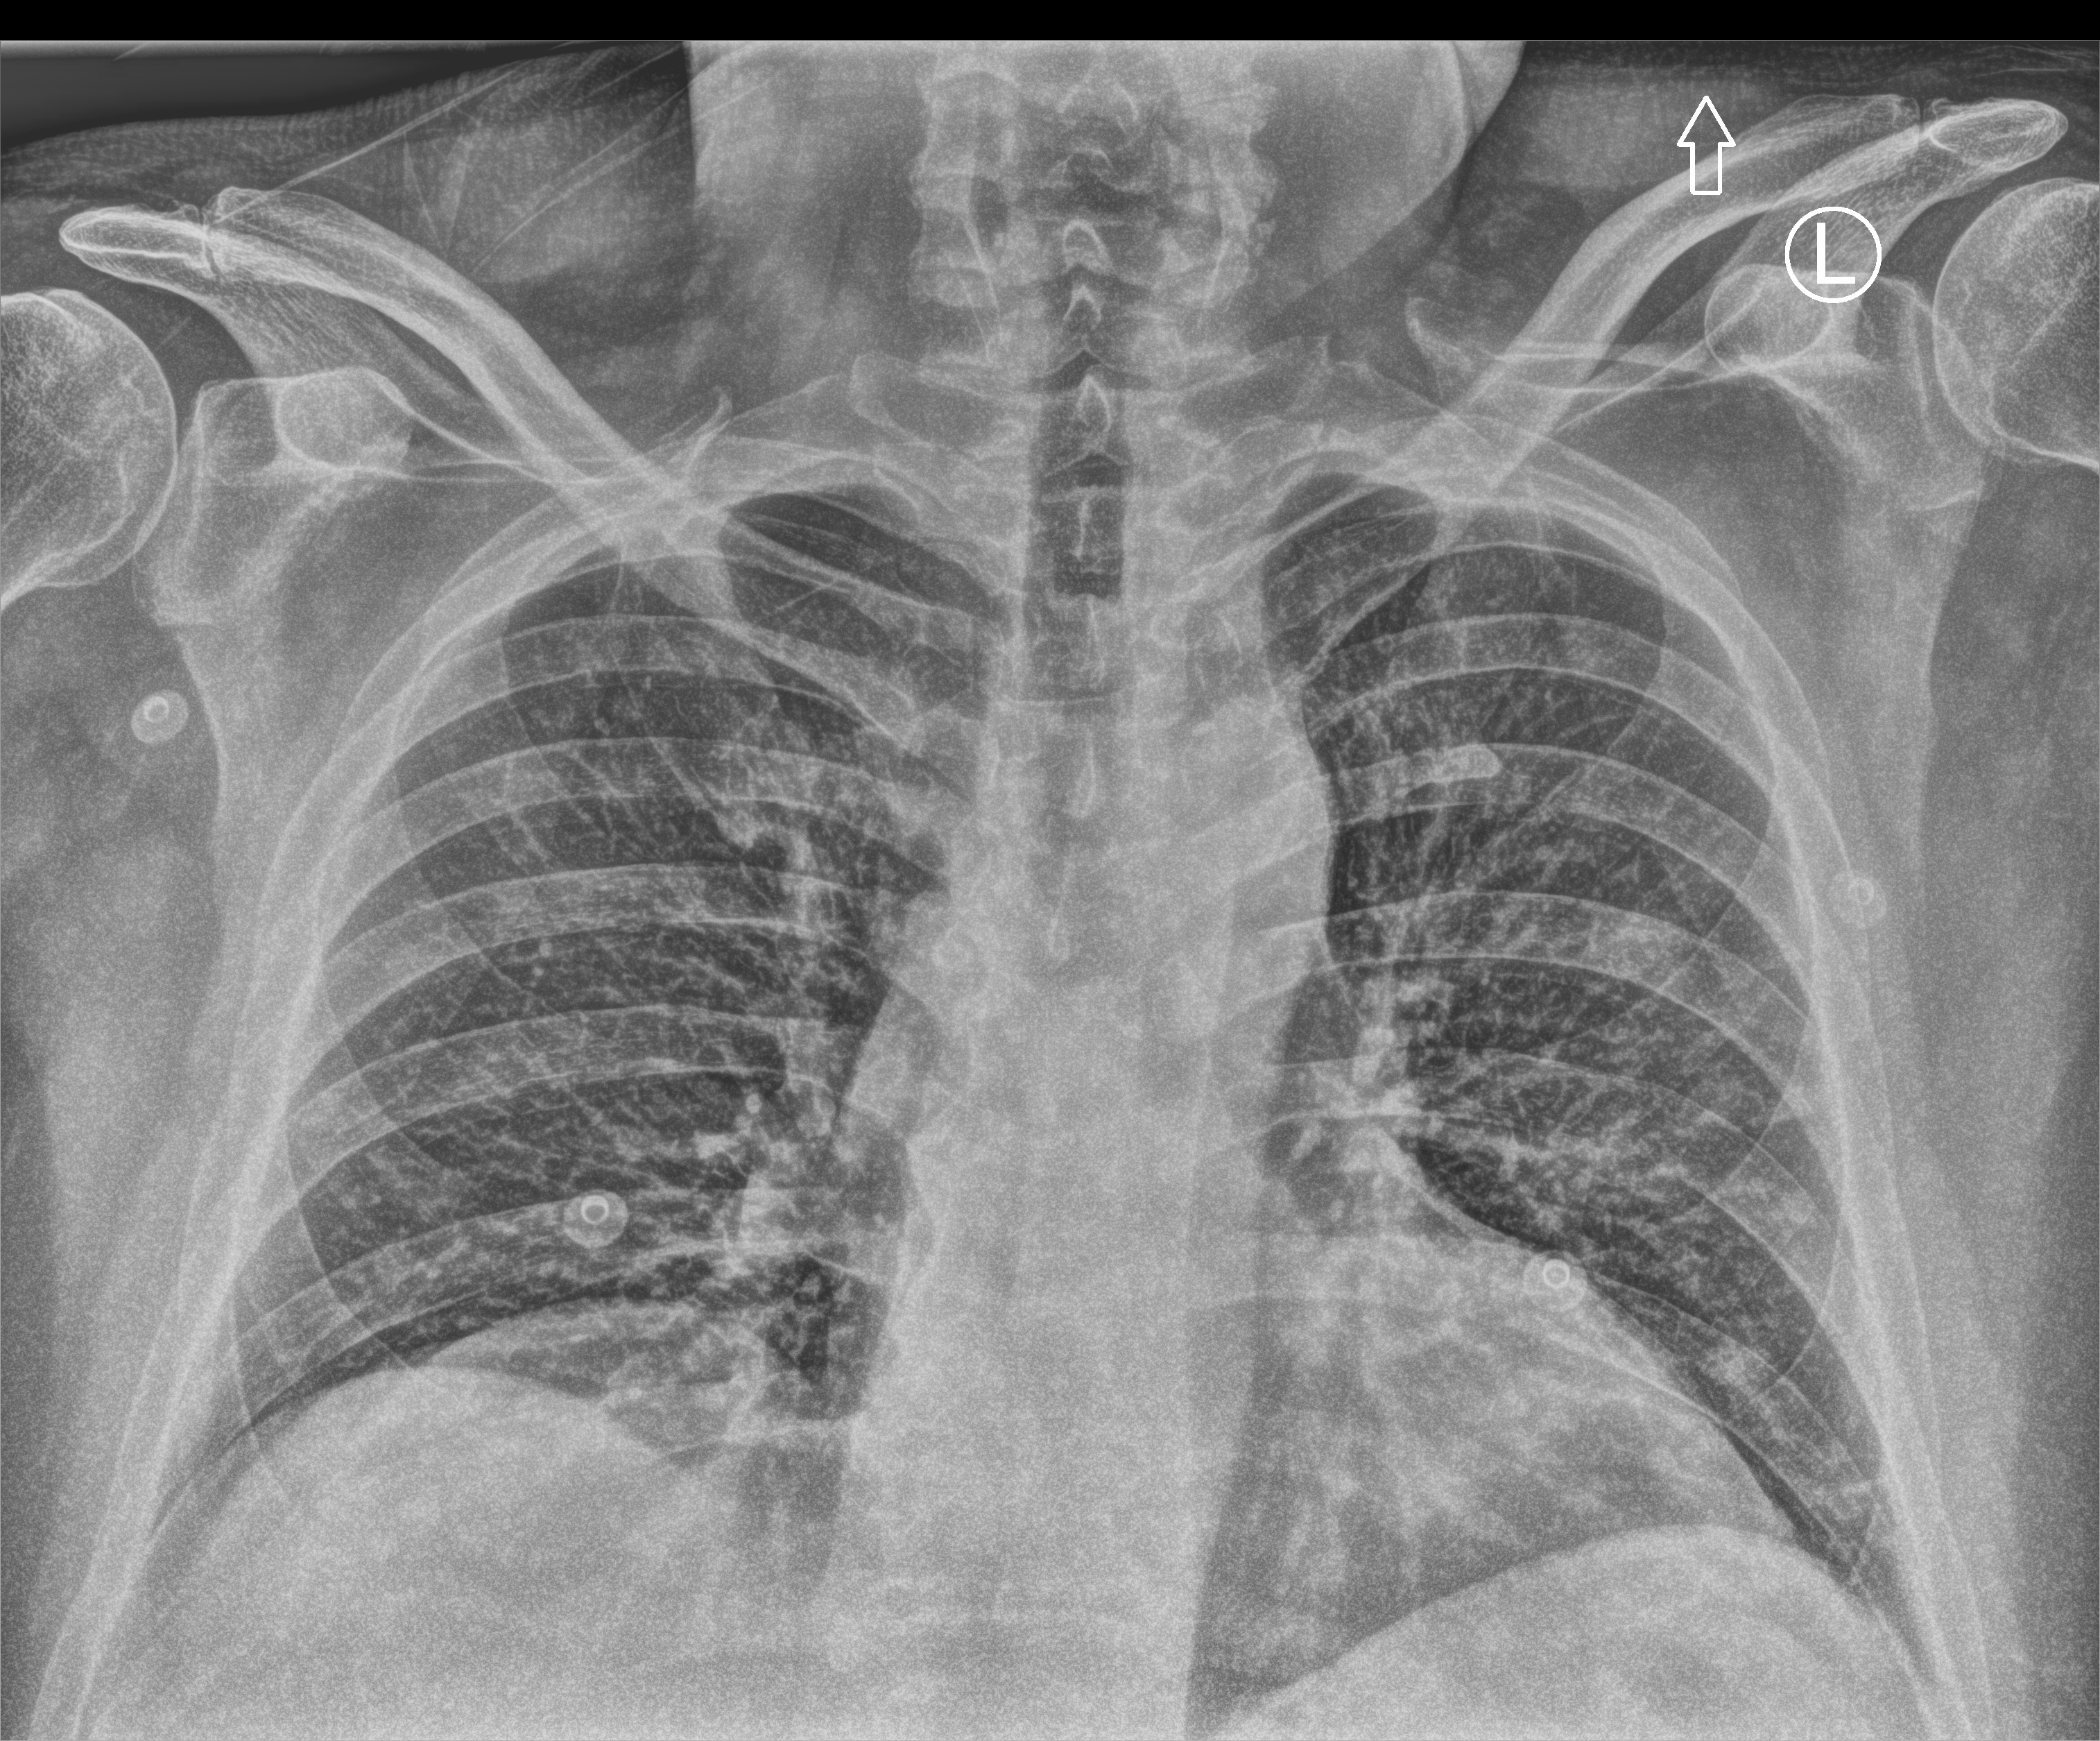
Chest X-ray (portable), anteroposterior (AP) projection. Male patient hospitalised with COVID-19, age 18–59 years.
Hospital-stay facts (about this admission, not read from this image; timing relative to this image not recorded):
- chronic kidney disease (admission record): no